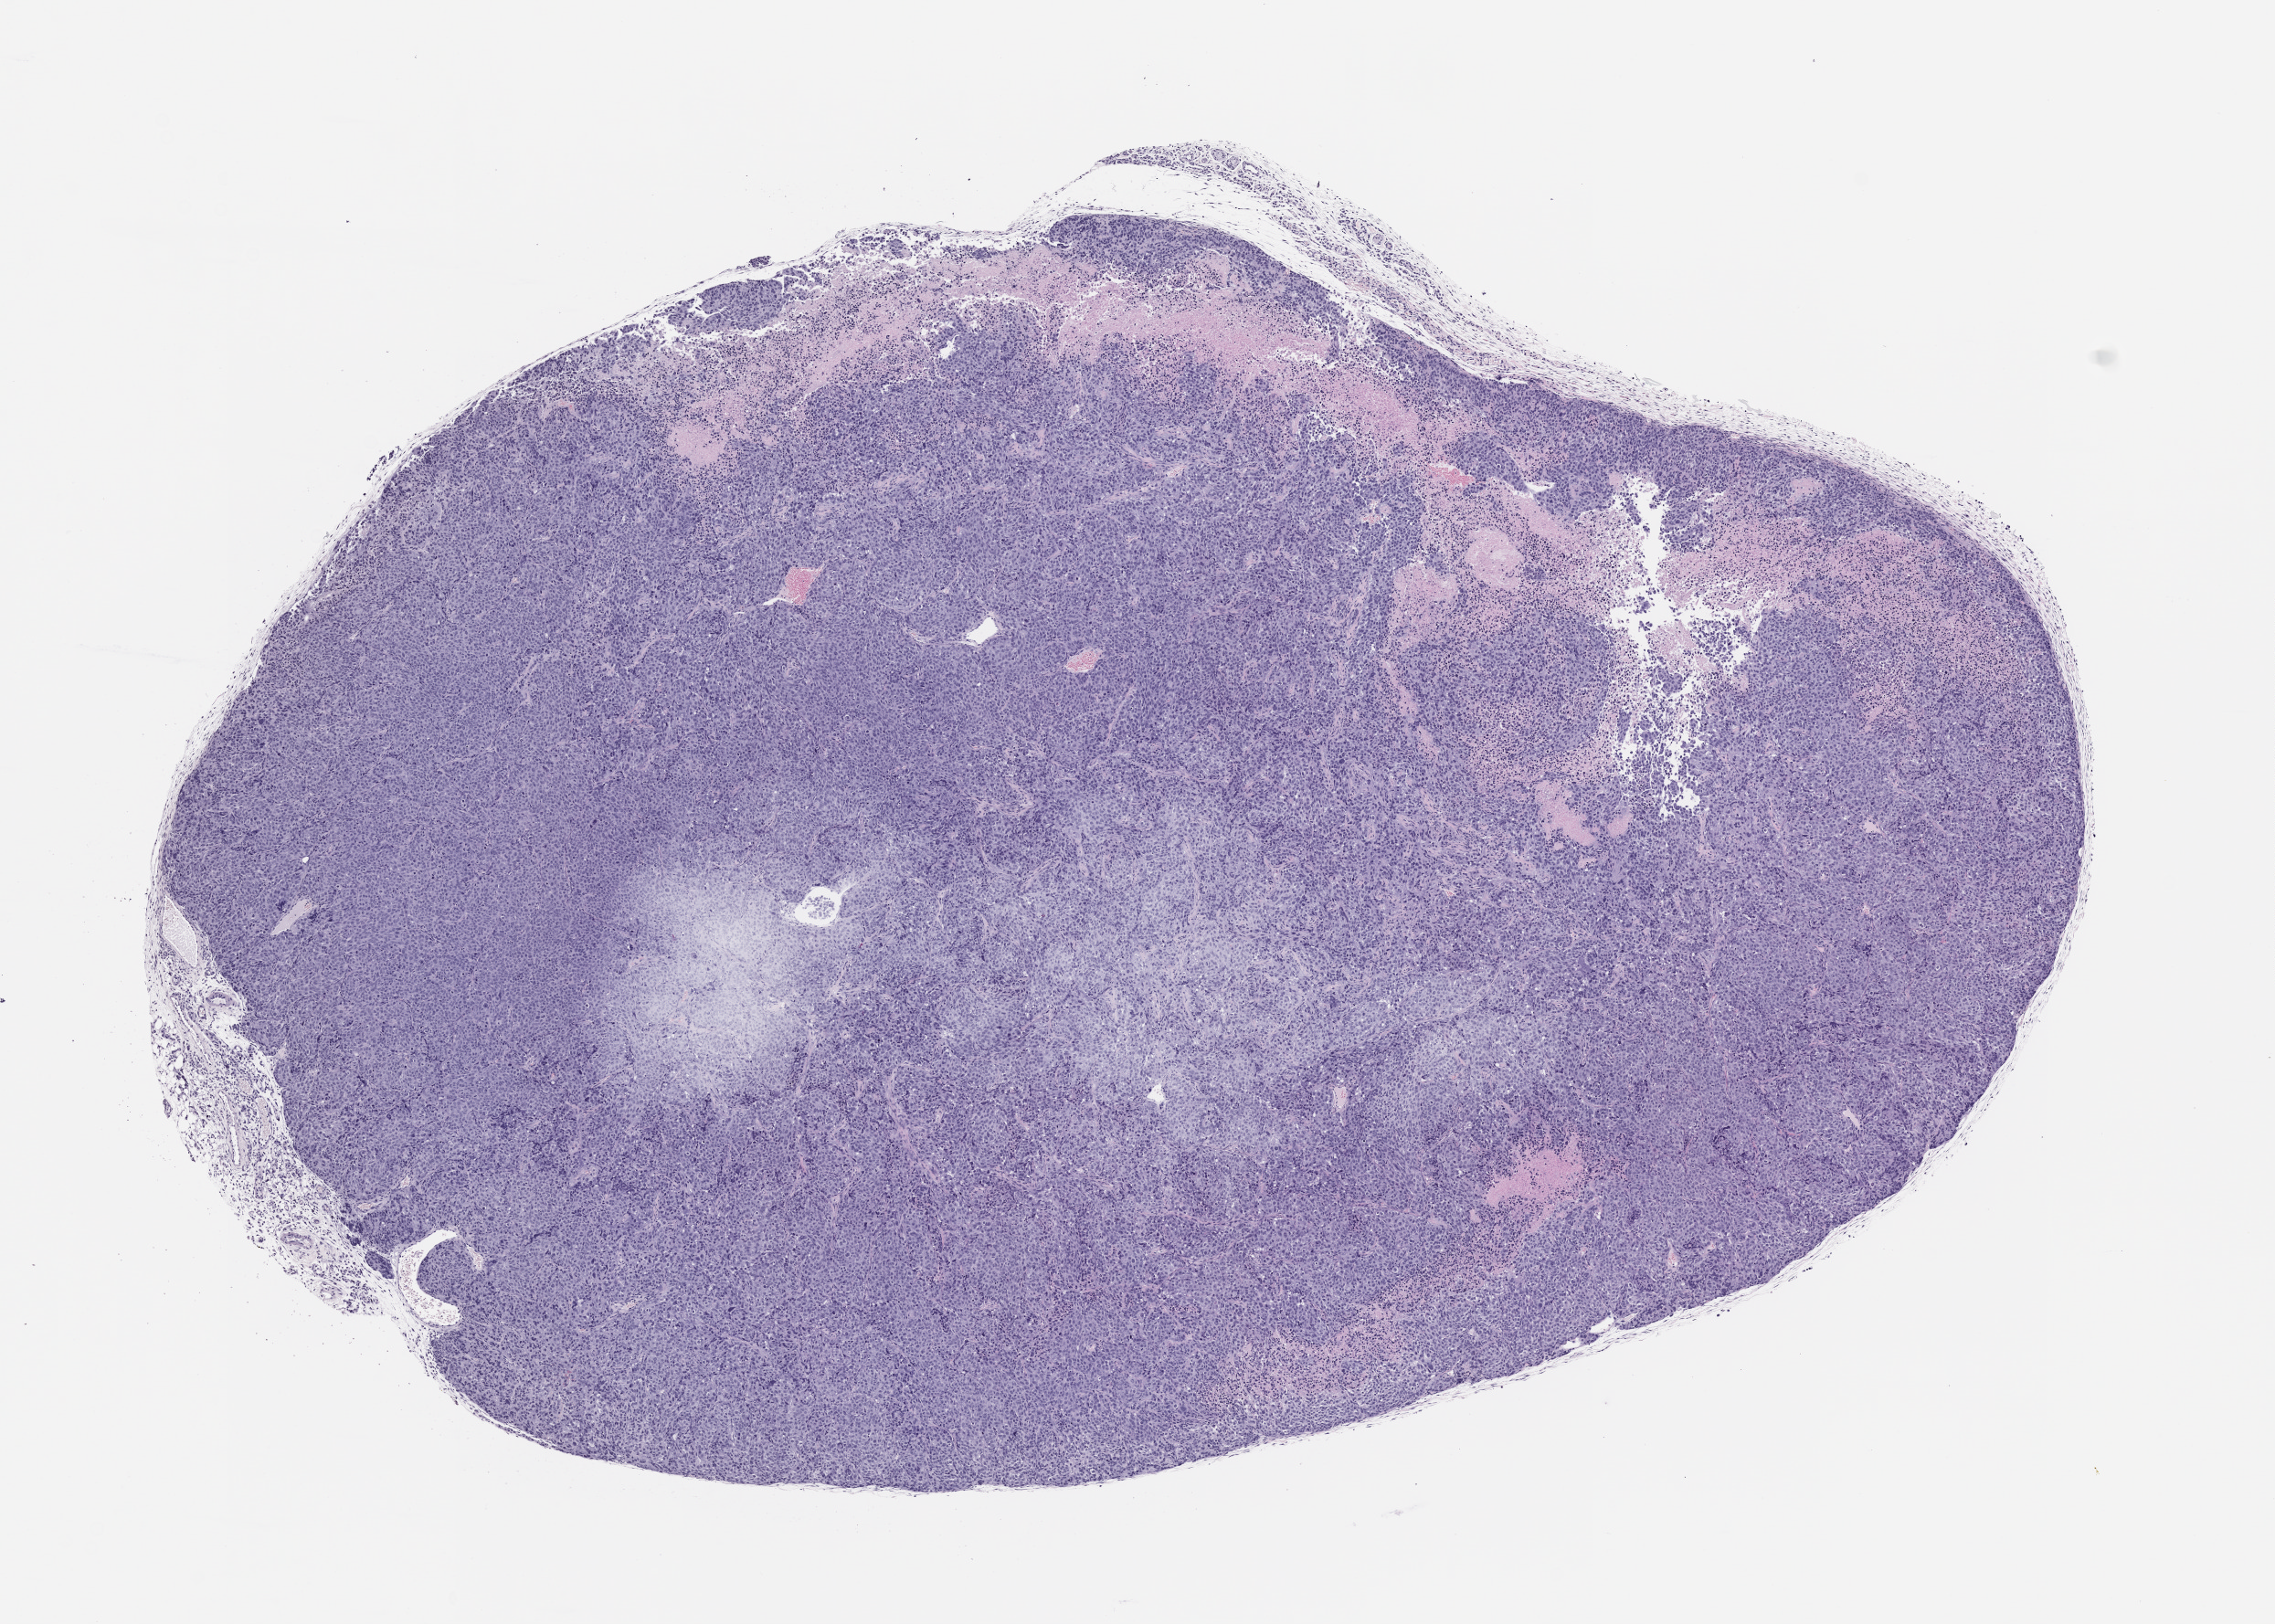
Whole-slide image, H&E: patient-derived xenograft (human tumor grown in a mouse), passage 0 — a low-resolution overview of the entire scanned area, about 10.0 x 7.2 mm. Formalin-fixed, paraffin-embedded (FFPE) tissue. Originating tumor site category: lung.
Originating patient diagnosis: Lung Squamous Cell Carcinoma.